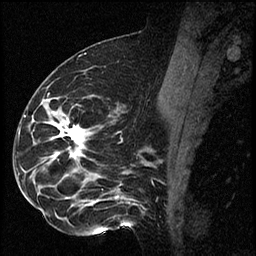
Breast MRI (dynamic contrast-enhanced), one sagittal slice. Position 37 of 60 along the scan axis. Dynamic contrast-enhanced series, image 2 of 2 at this slice position (ordered by acquisition). 1.5 T. TE 4.2 ms, TR 17.3 ms. 256 × 256 image matrix, field of view 200 × 200 mm. Female patient. Case-level facts recorded for this patient, not image findings: setting: breast cancer imaged before/during neoadjuvant chemotherapy; receptor status: HR-positive, HER2-negative.
Structures marked on this image (semi-automatic segmentation, software-assisted and operator-edited):
- analysis volume of interest (the breast-tissue region the enhancement analysis was run in; not a lesion): bounding box [x1, y1, x2, y2] px = [41, 96, 115, 223]
- tumour enhancement mask (voxels above the 100 % enhancement threshold inside the analysis volume of interest): [58, 124, 84, 156]